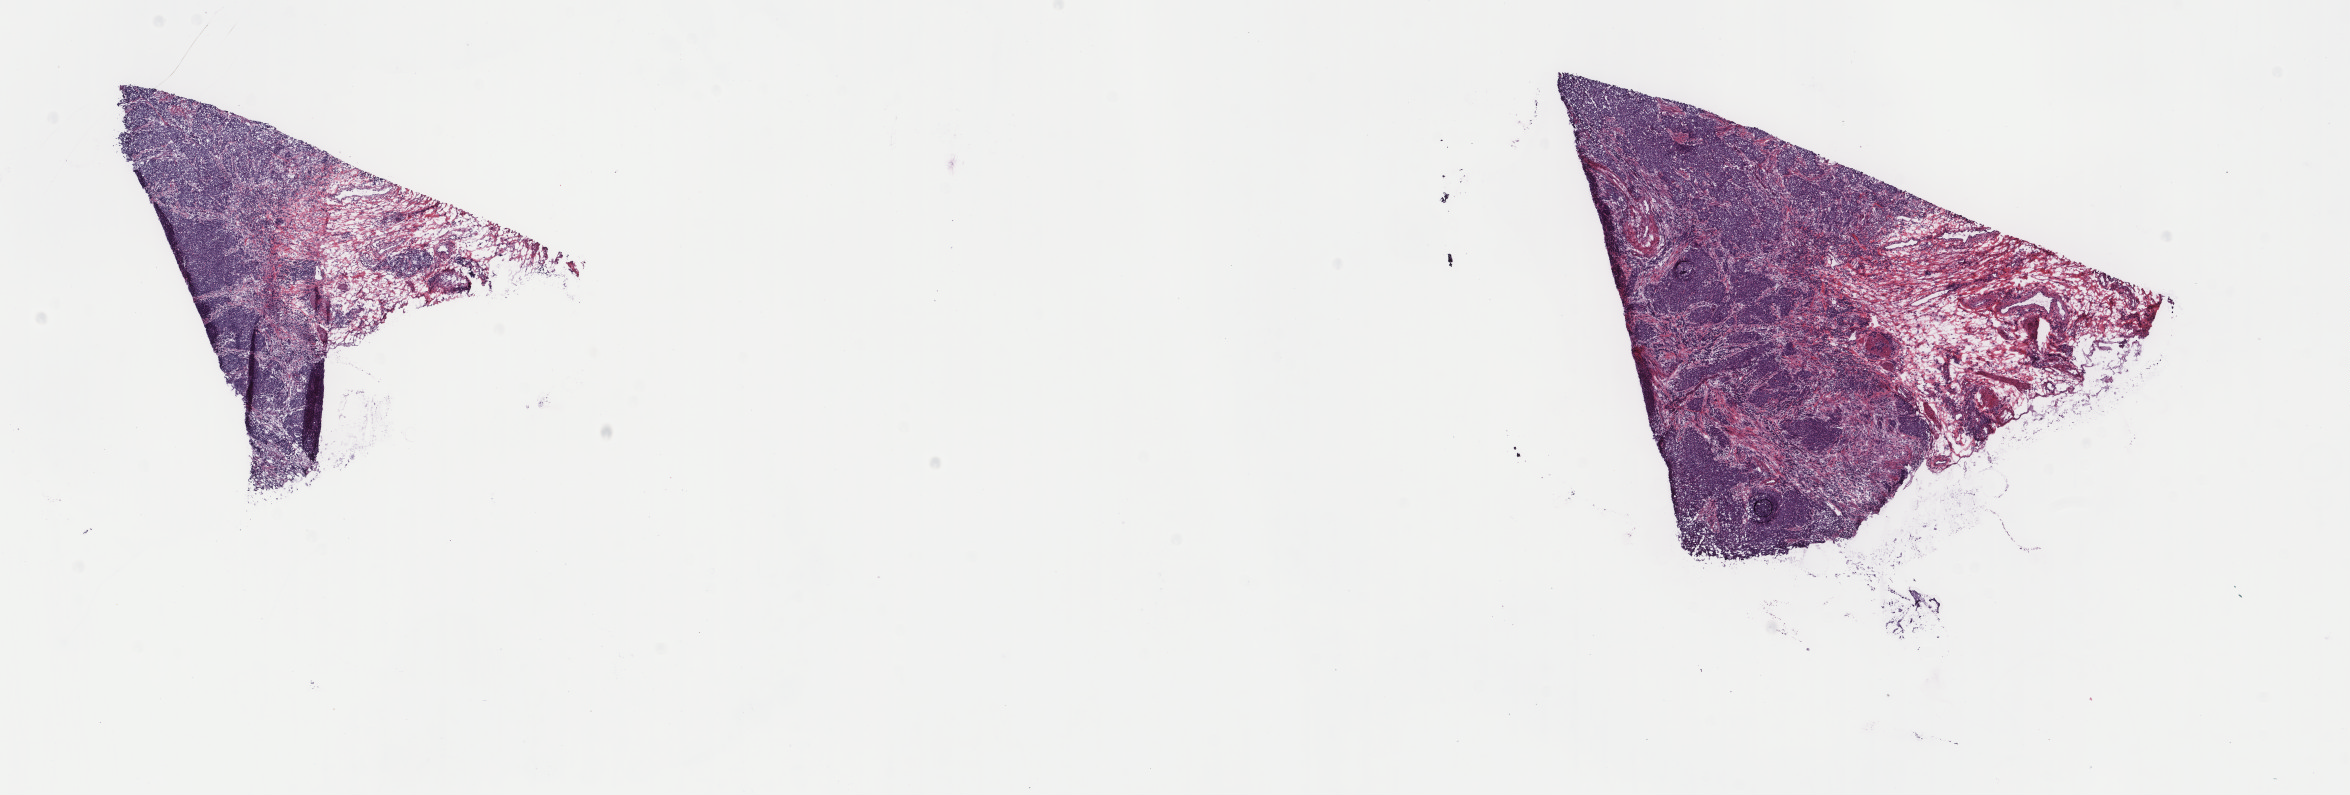
Whole-slide histology image, Hematoxylin and eosin (H&E) stained — shown as a low-resolution overview of the whole scanned area (about 18.7 x 6.3 mm, acquisition: 40x scan); frozen section from the top of the tissue portion; esophagus, primary tumour sample. Patient: male, age at initial diagnosis 52 years. Histologic grade: G2 (moderately differentiated). Pathologist review of this section (percent, as recorded): tumour cells 75%, tumour nuclei 75%, normal cells 0%, stromal cells 25%, necrosis 0%. Infiltration values recorded for this section: lymphocyte infiltration 5%, monocyte infiltration 2%, neutrophil infiltration 2%.
* pathologic diagnosis: Squamous cell carcinoma, NOS (middle third of esophagus)
* AJCC pathologic stage: IIA (6th edition)